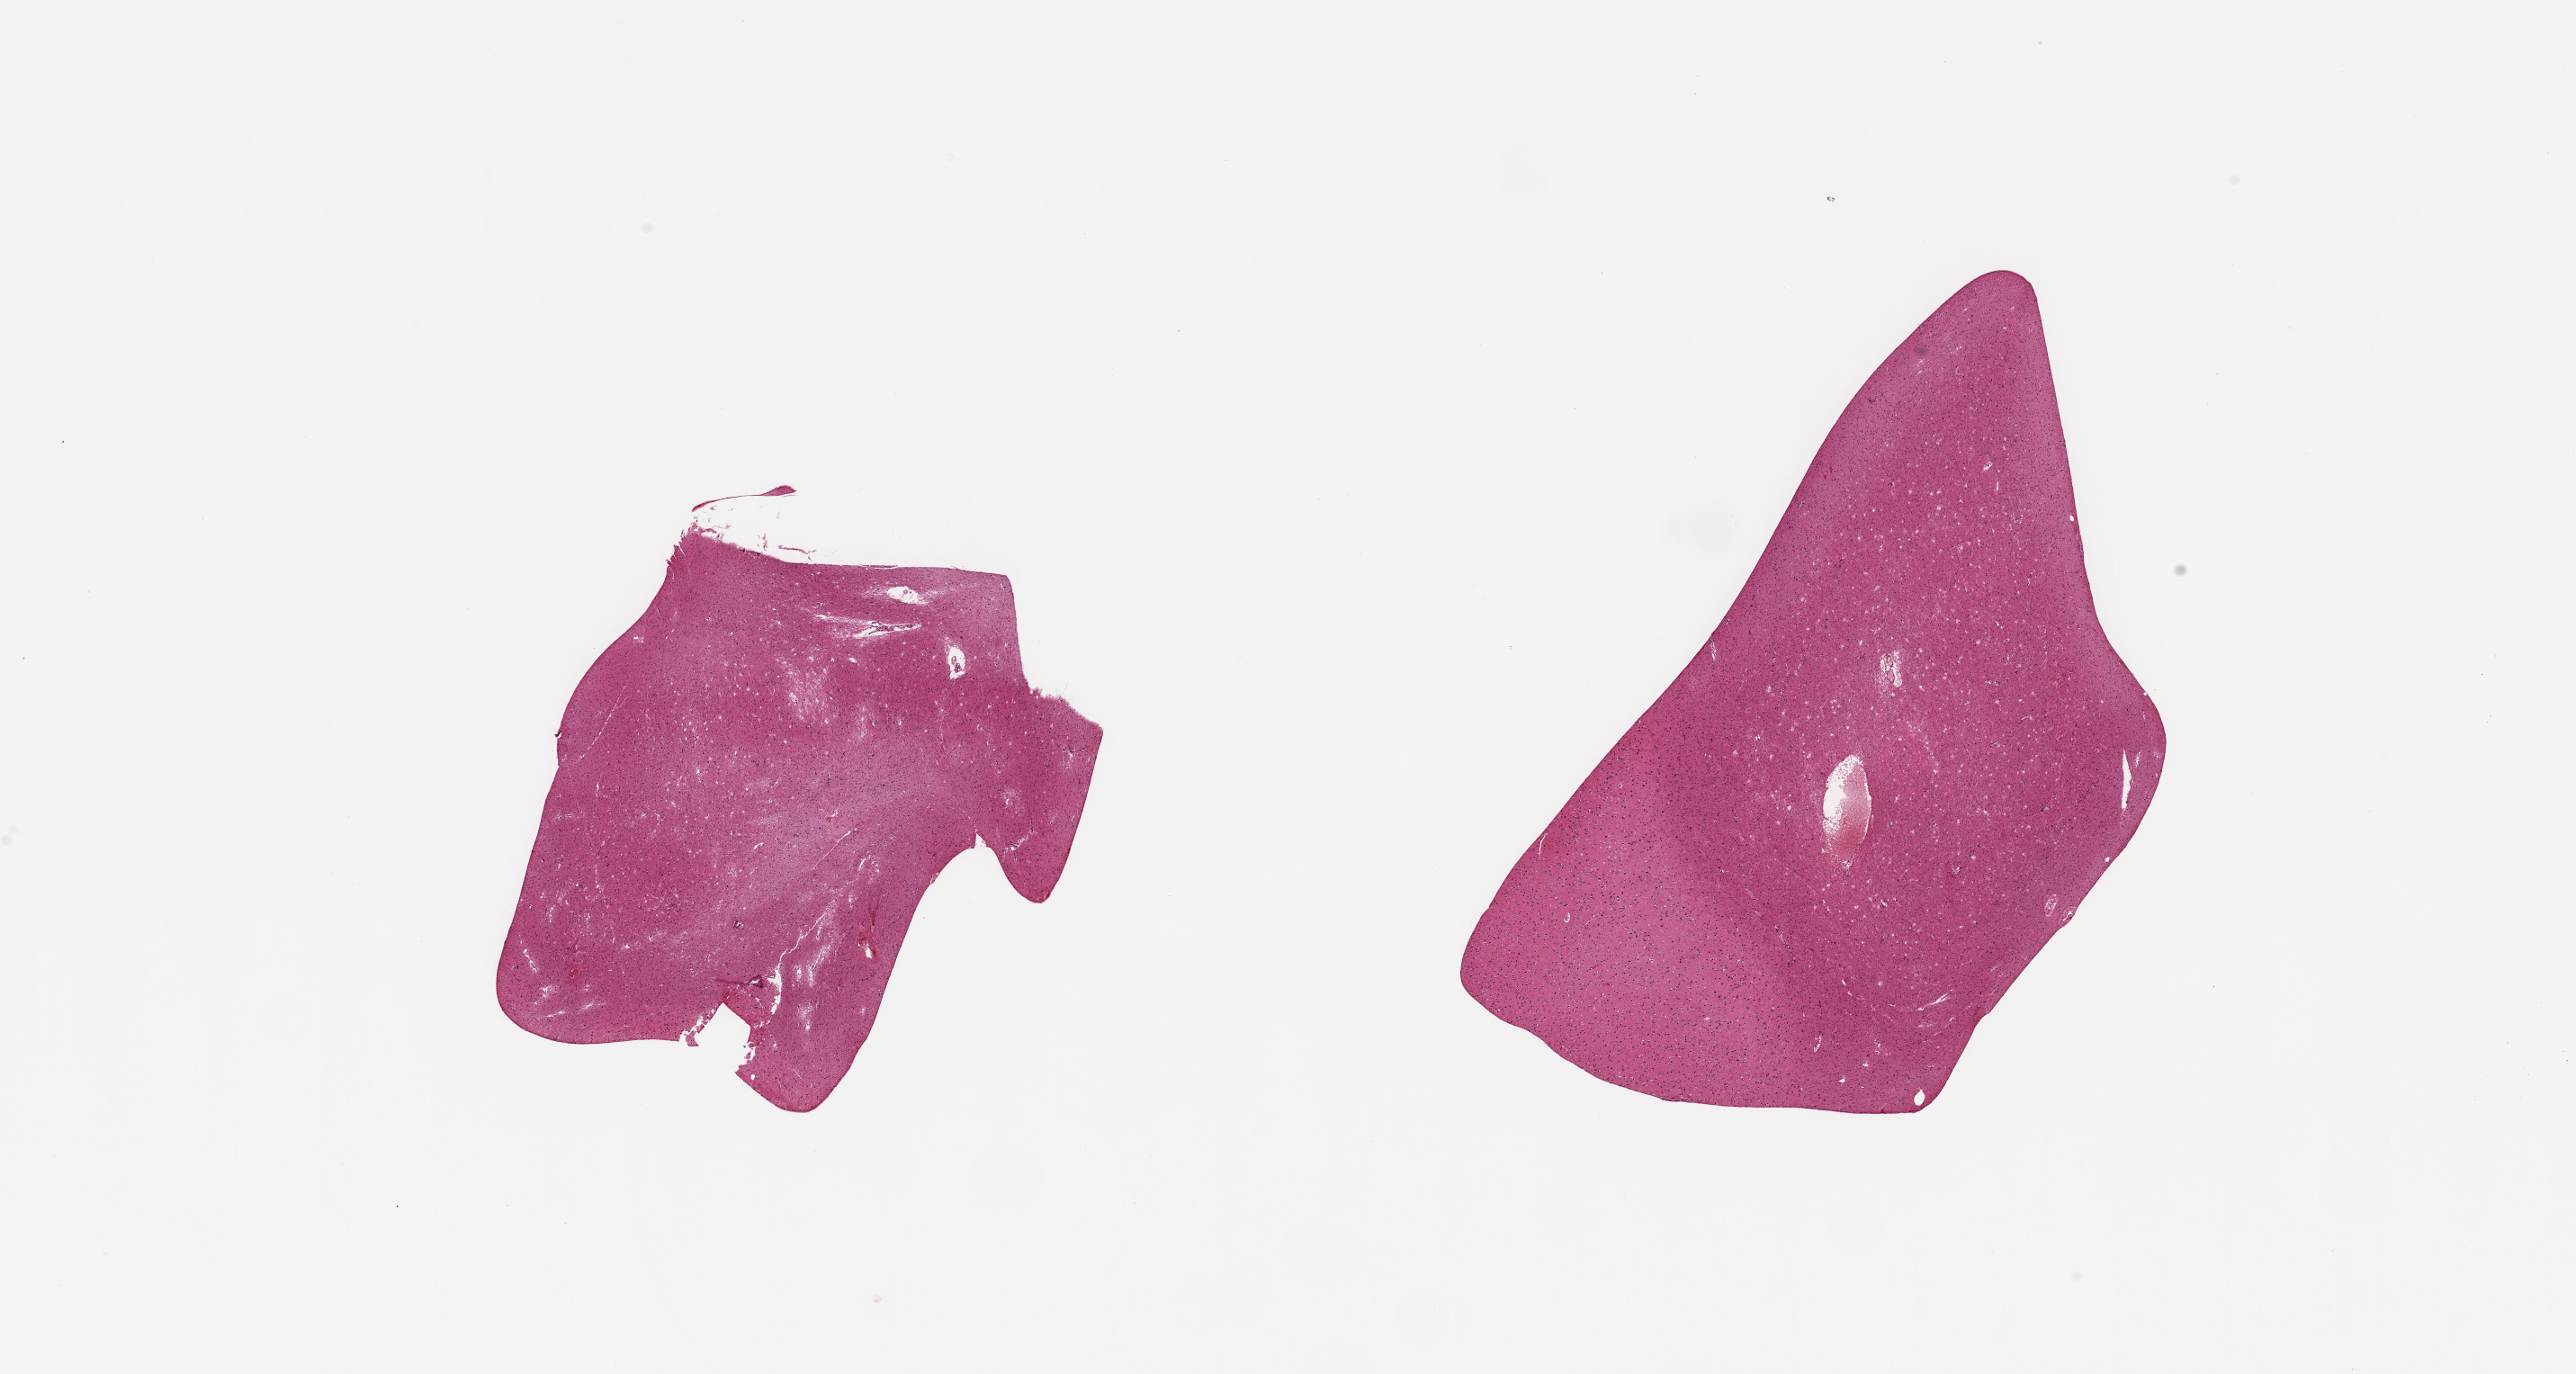
Digitized H&E-stained section — shown as a low-resolution overview of the whole scanned area (about 22.6 x 12.1 mm); PAXgene-fixed paraffin-embedded (PFPE) section; target tissue: cerebral cortex; donor tissue sample. Donor sex: male.
- review note (as recorded): 2 pieces, no abnormalities